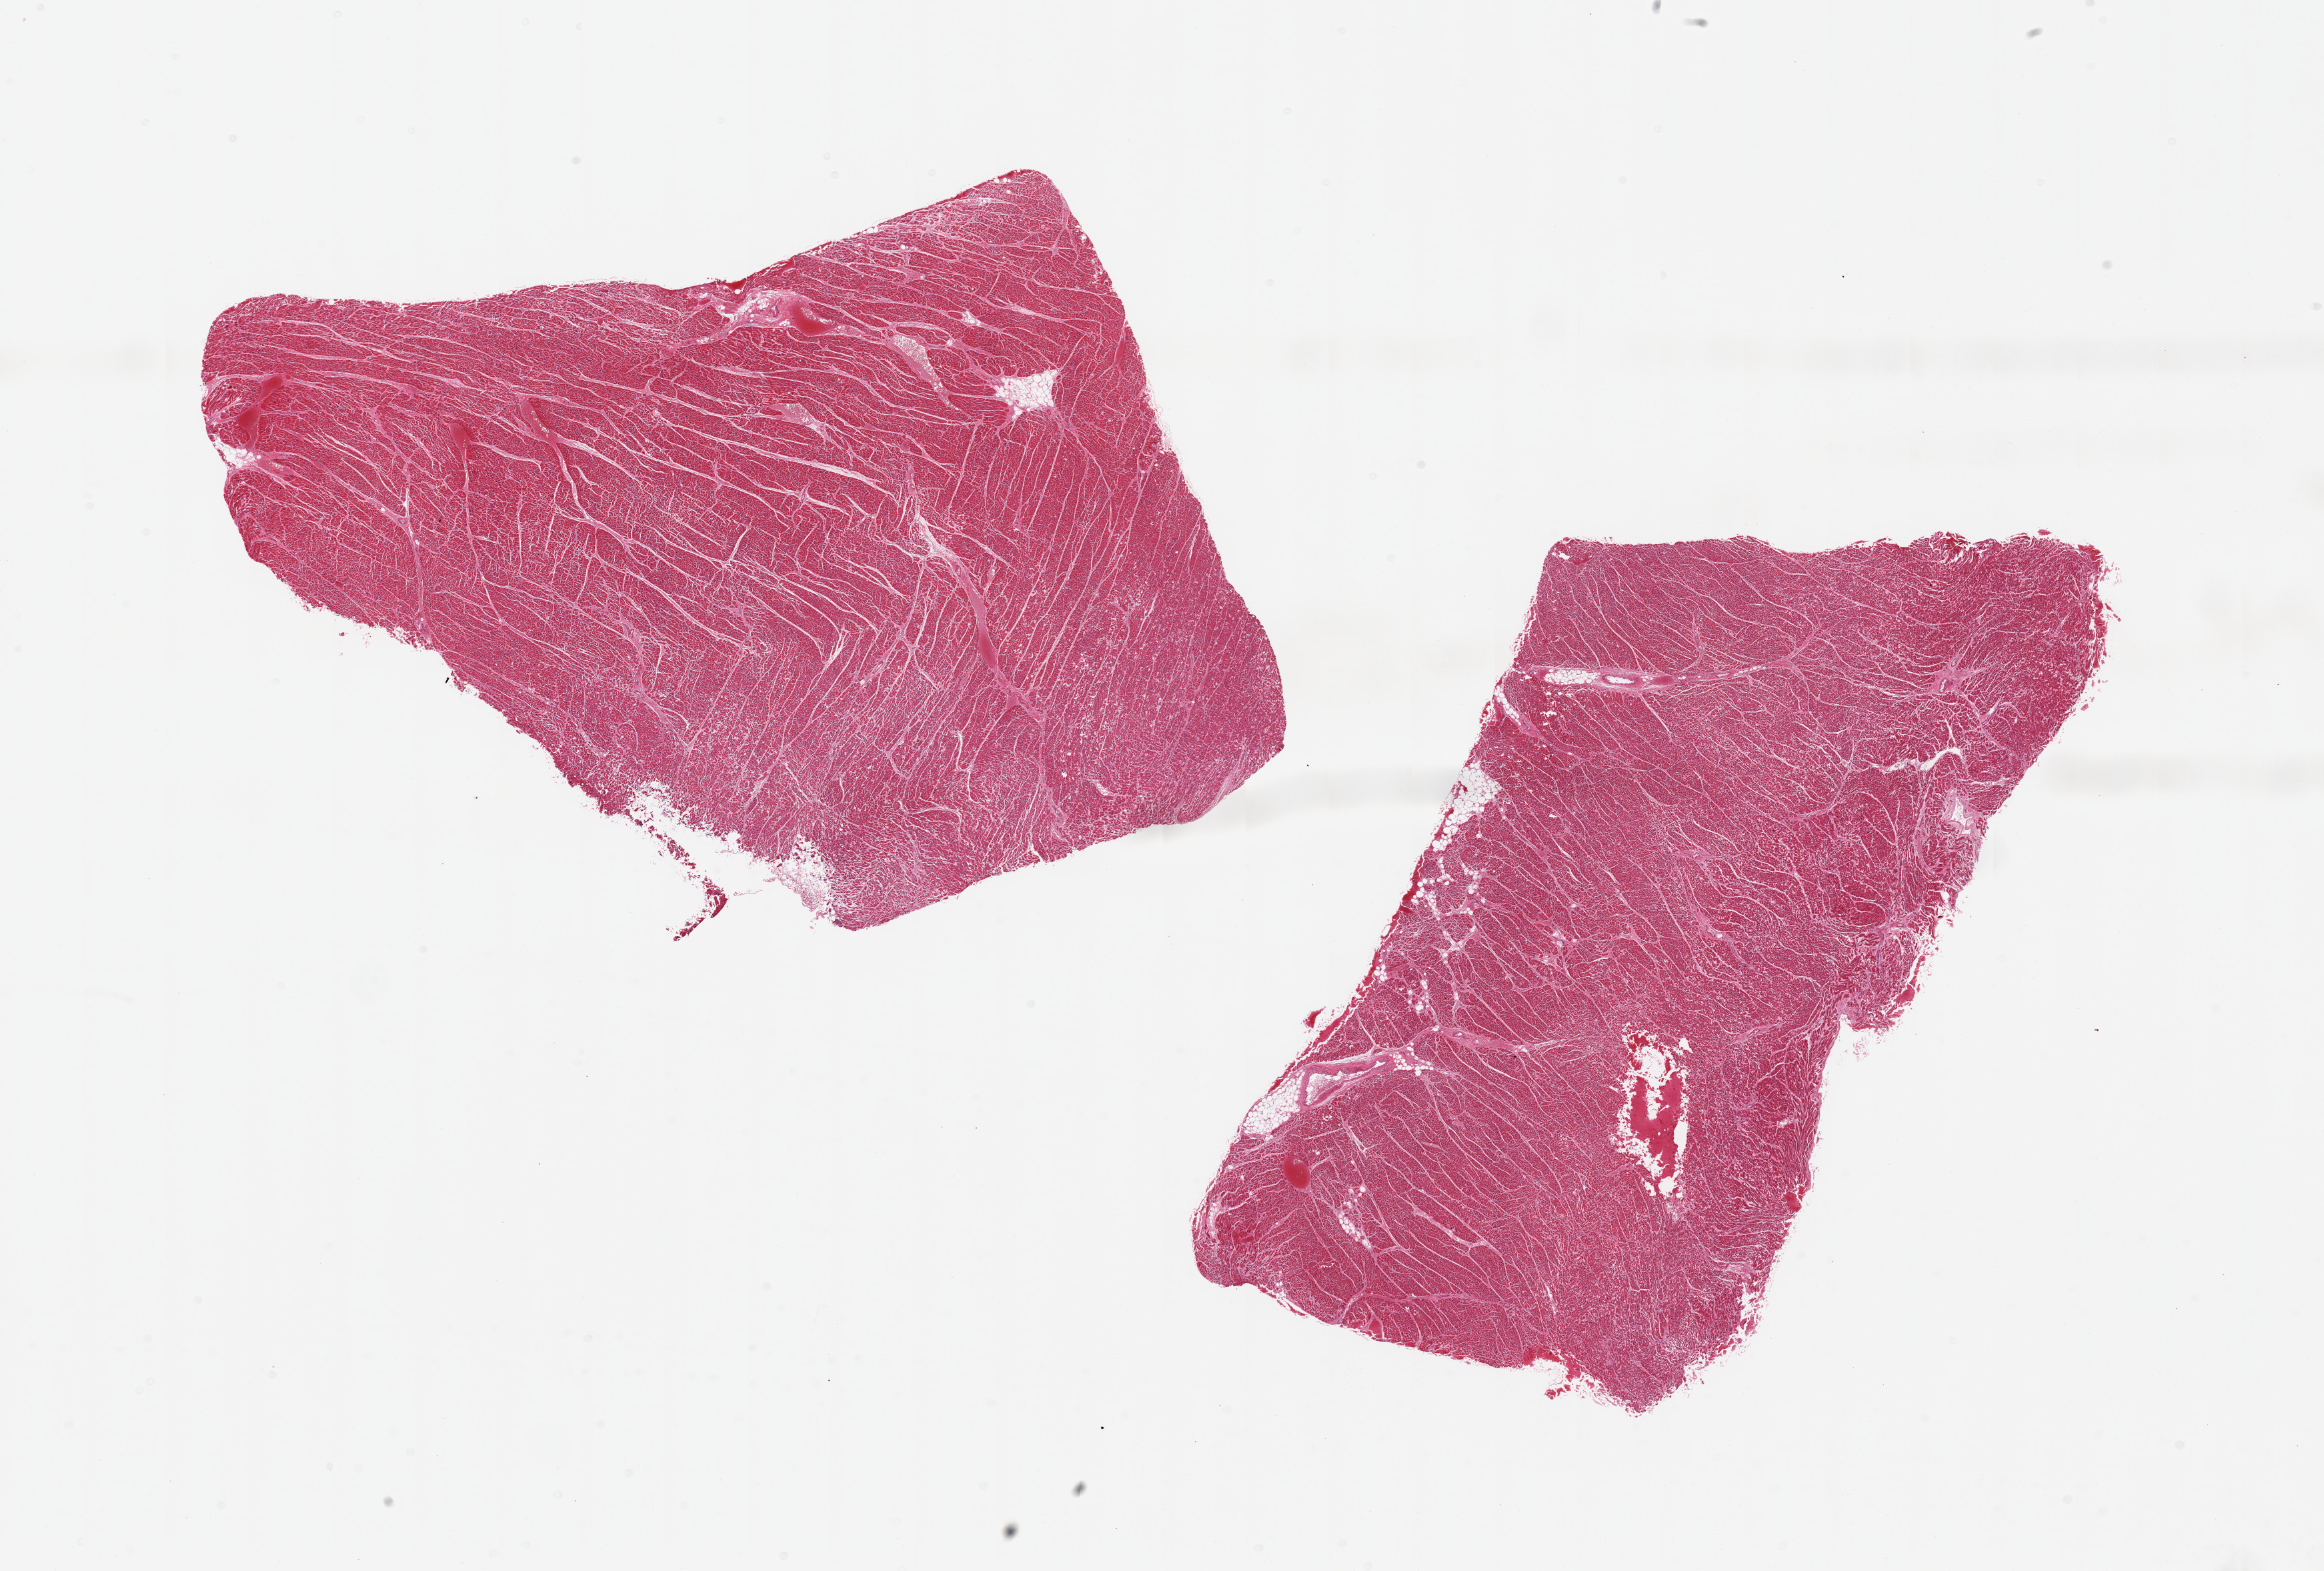
Whole-slide image, hematoxylin and eosin (H&E) stain — shown as a low-resolution overview of the whole scanned area (about 27.6 x 18.6 mm, slide scanned at 20x), PAXgene-fixed paraffin-embedded (PFPE) section, sampled site (target tissue): heart, tissue donor sample. Donor sex: male.
* review note (as recorded): 2 pieces; no fibrosis; <5% internal fat